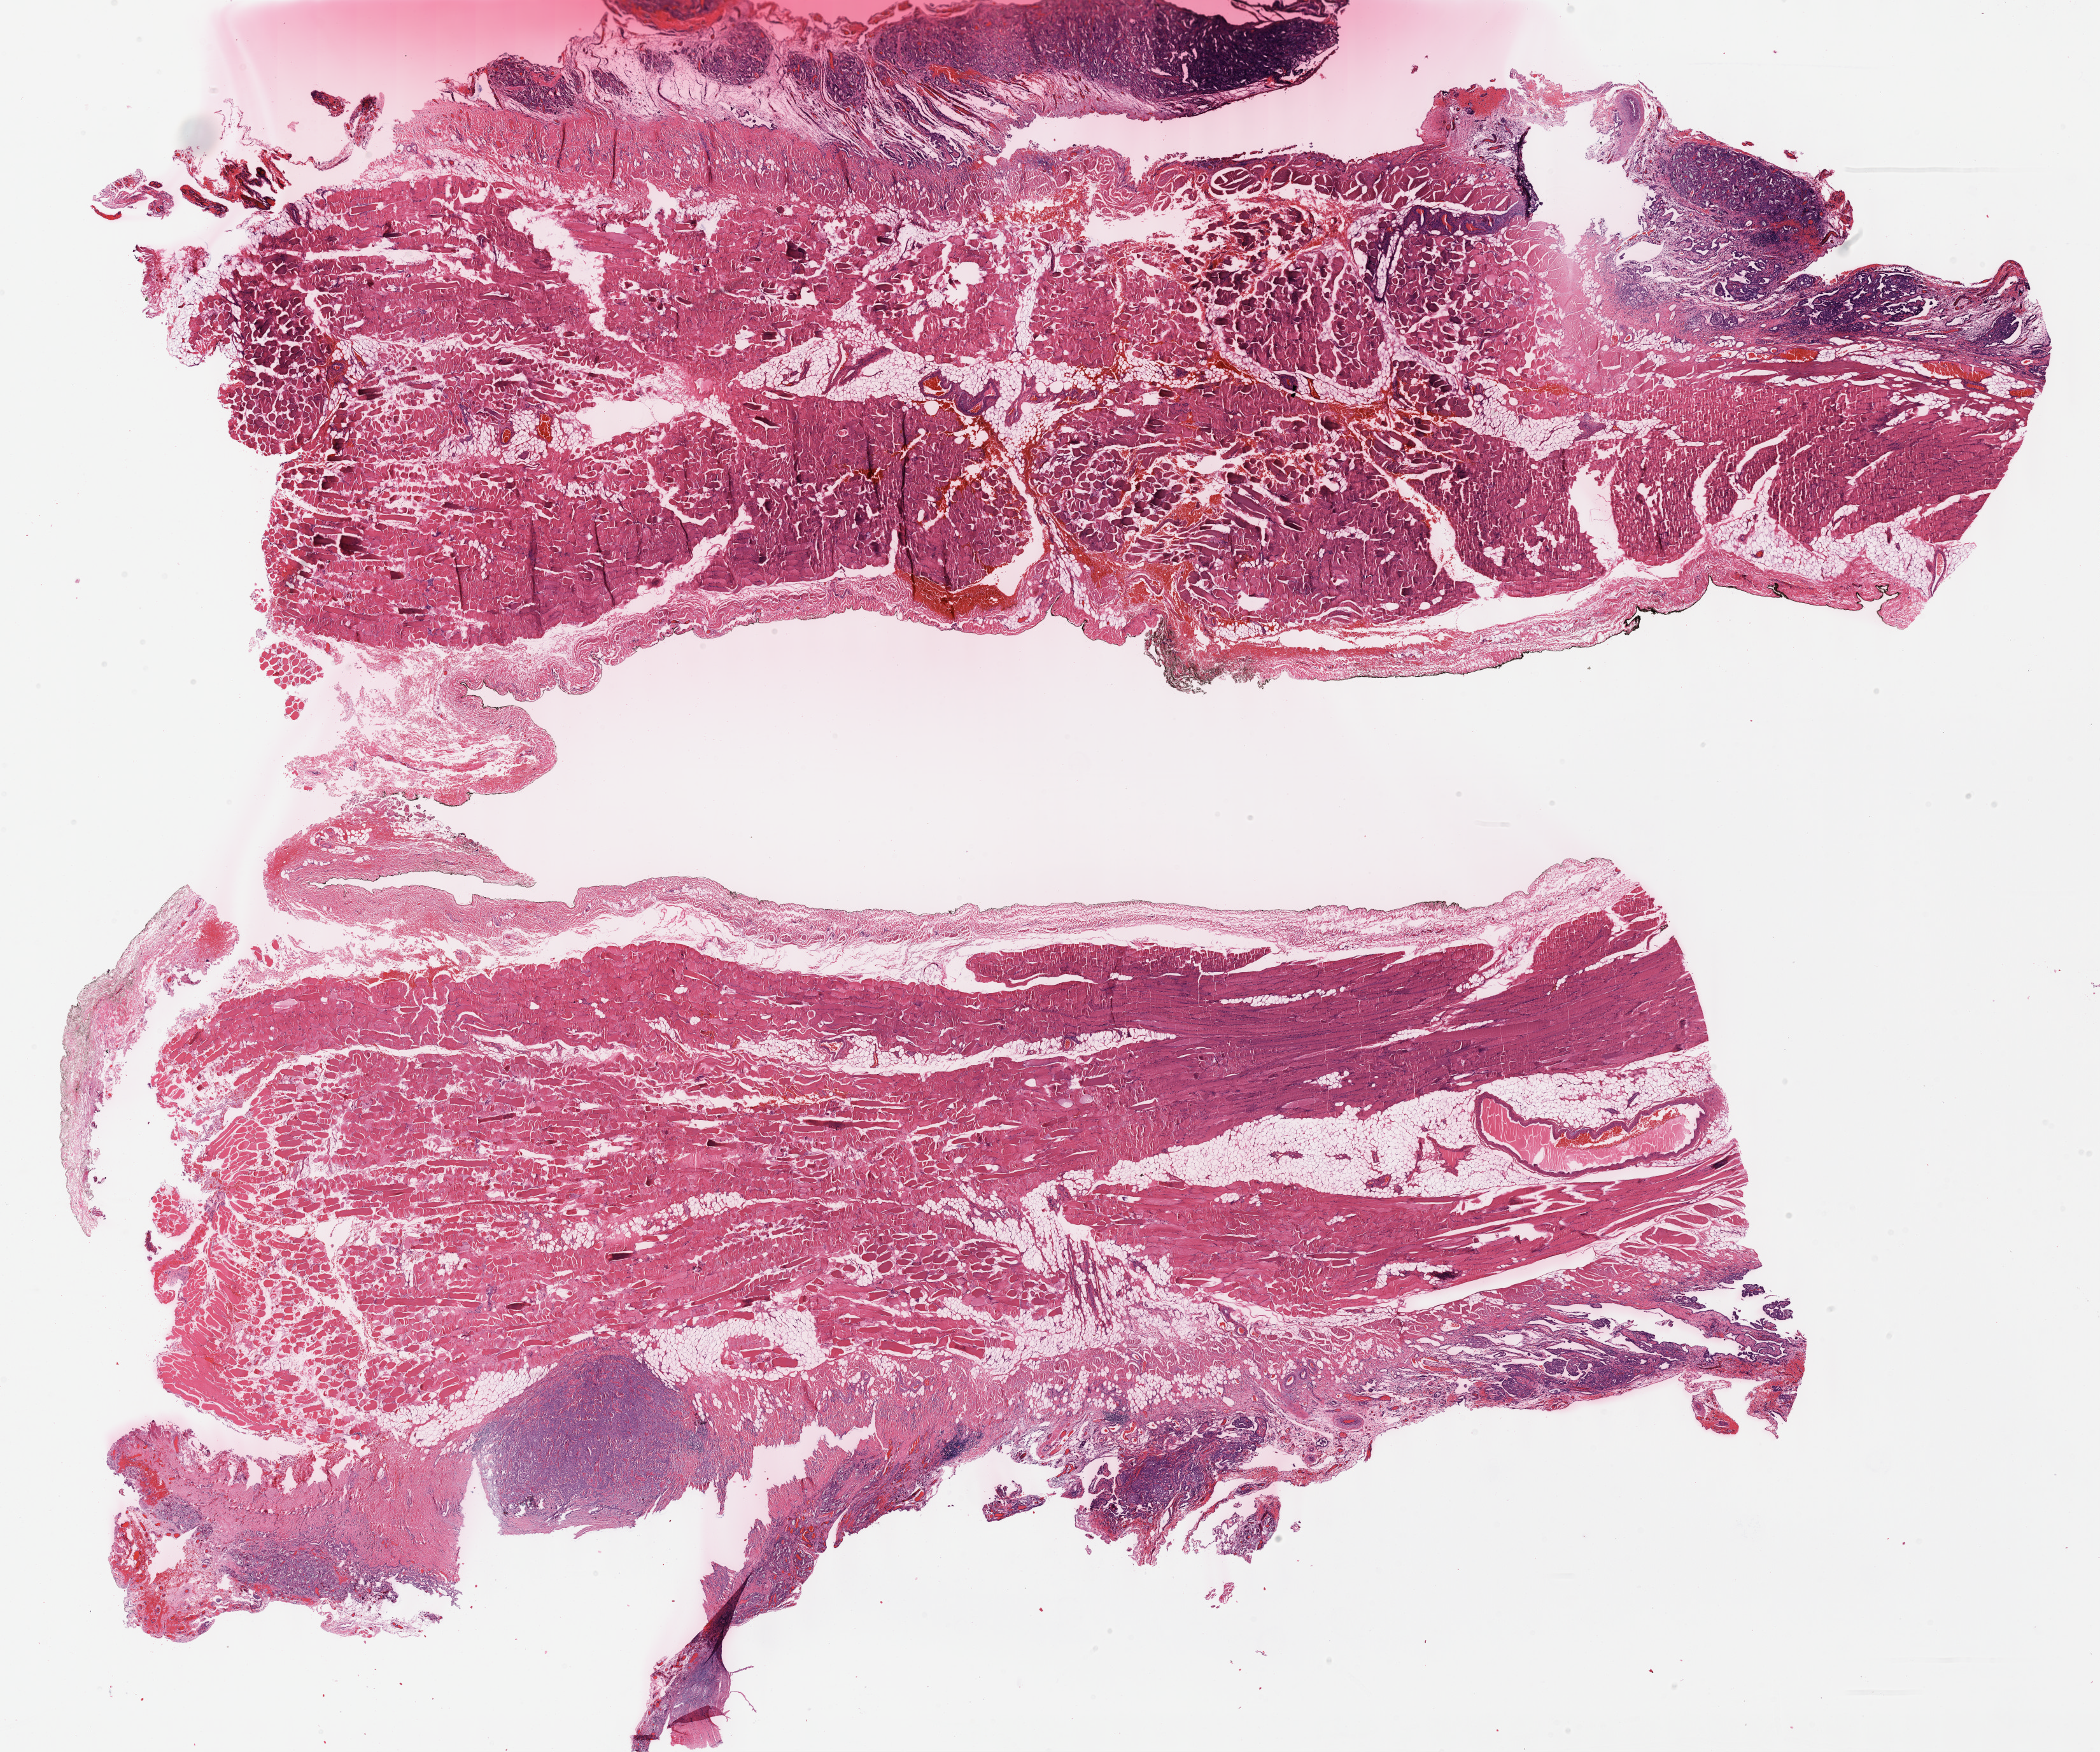
Hematoxylin and eosin (H&E) stained whole-slide image, whole scanned area (about 26.7 x 22.2 mm, slide scanned at 40x) shown as a low-resolution overview; formalin-fixed paraffin-embedded (FFPE) diagnostic section; primary tumour sample from the mesothelium. Patient: male, age at initial diagnosis 56 years.
Pathologic diagnosis: Epithelioid mesothelioma, malignant.